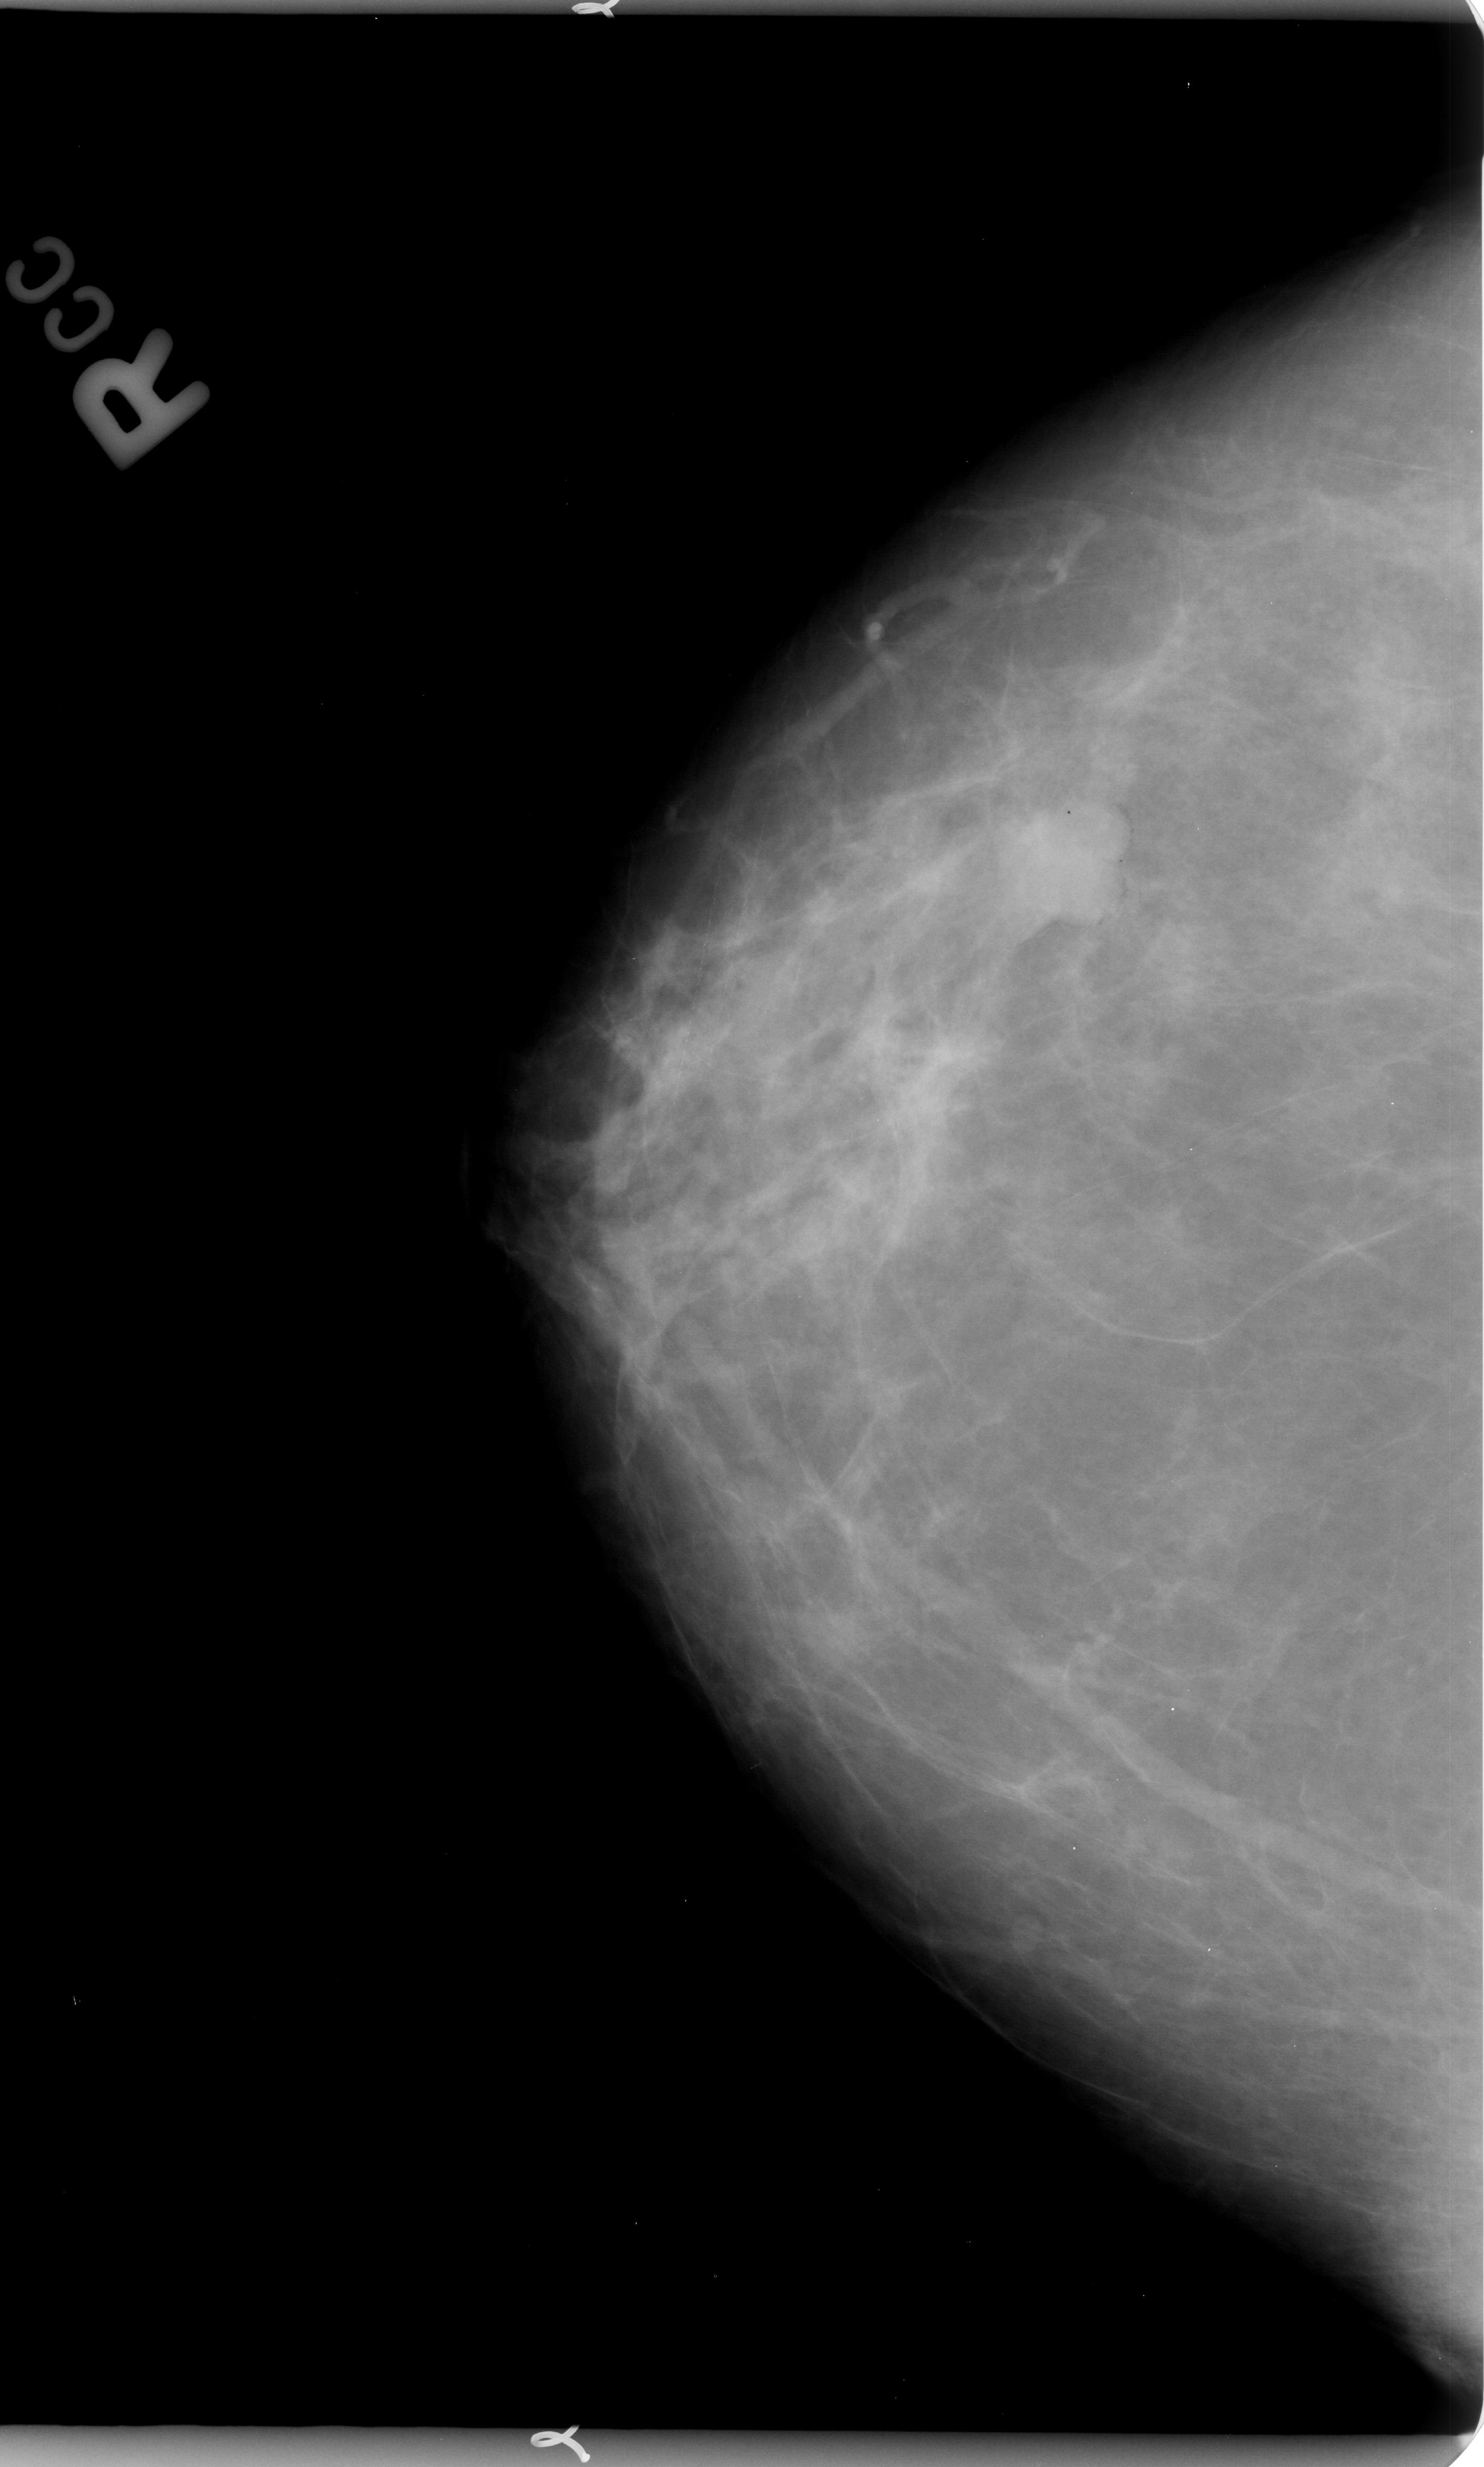
Scanned film-screen mammogram. Right breast. Craniocaudal (CC) view. BI-RADS breast density category 2 (scale 1–4). 1484 × 2467 image matrix.
Marked abnormalities (boxes around the expert regions of interest):
- mass, shape lobulated, margins circumscribed / ill defined; BI-RADS assessment category 4; pathology (as recorded): malignant: bounding box (x1, y1, x2, y2) in pixels: (994, 799, 1129, 932)